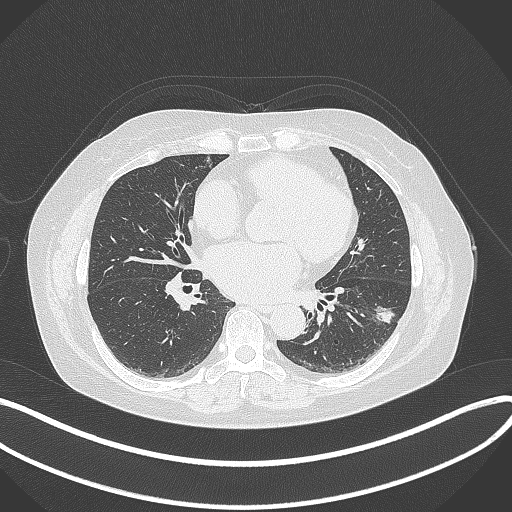
Chest CT, one axial slice; position 163 of 373 along the scan axis; lung window (W 1500 / L -600 HU); 1 mm slice thickness; 512 × 512 image matrix, field of view 400 × 400 mm. Female patient, age 67 years. From the clinical record (not read from this slice): clinical TNM (as recorded): T1c N0 M0.
Annotated regions visible in this slice (rectangle marked by the reading radiologist):
- lung tumour (recorded histology: adenocarcinoma): box from (x=370, y=297) to (x=399, y=332) px